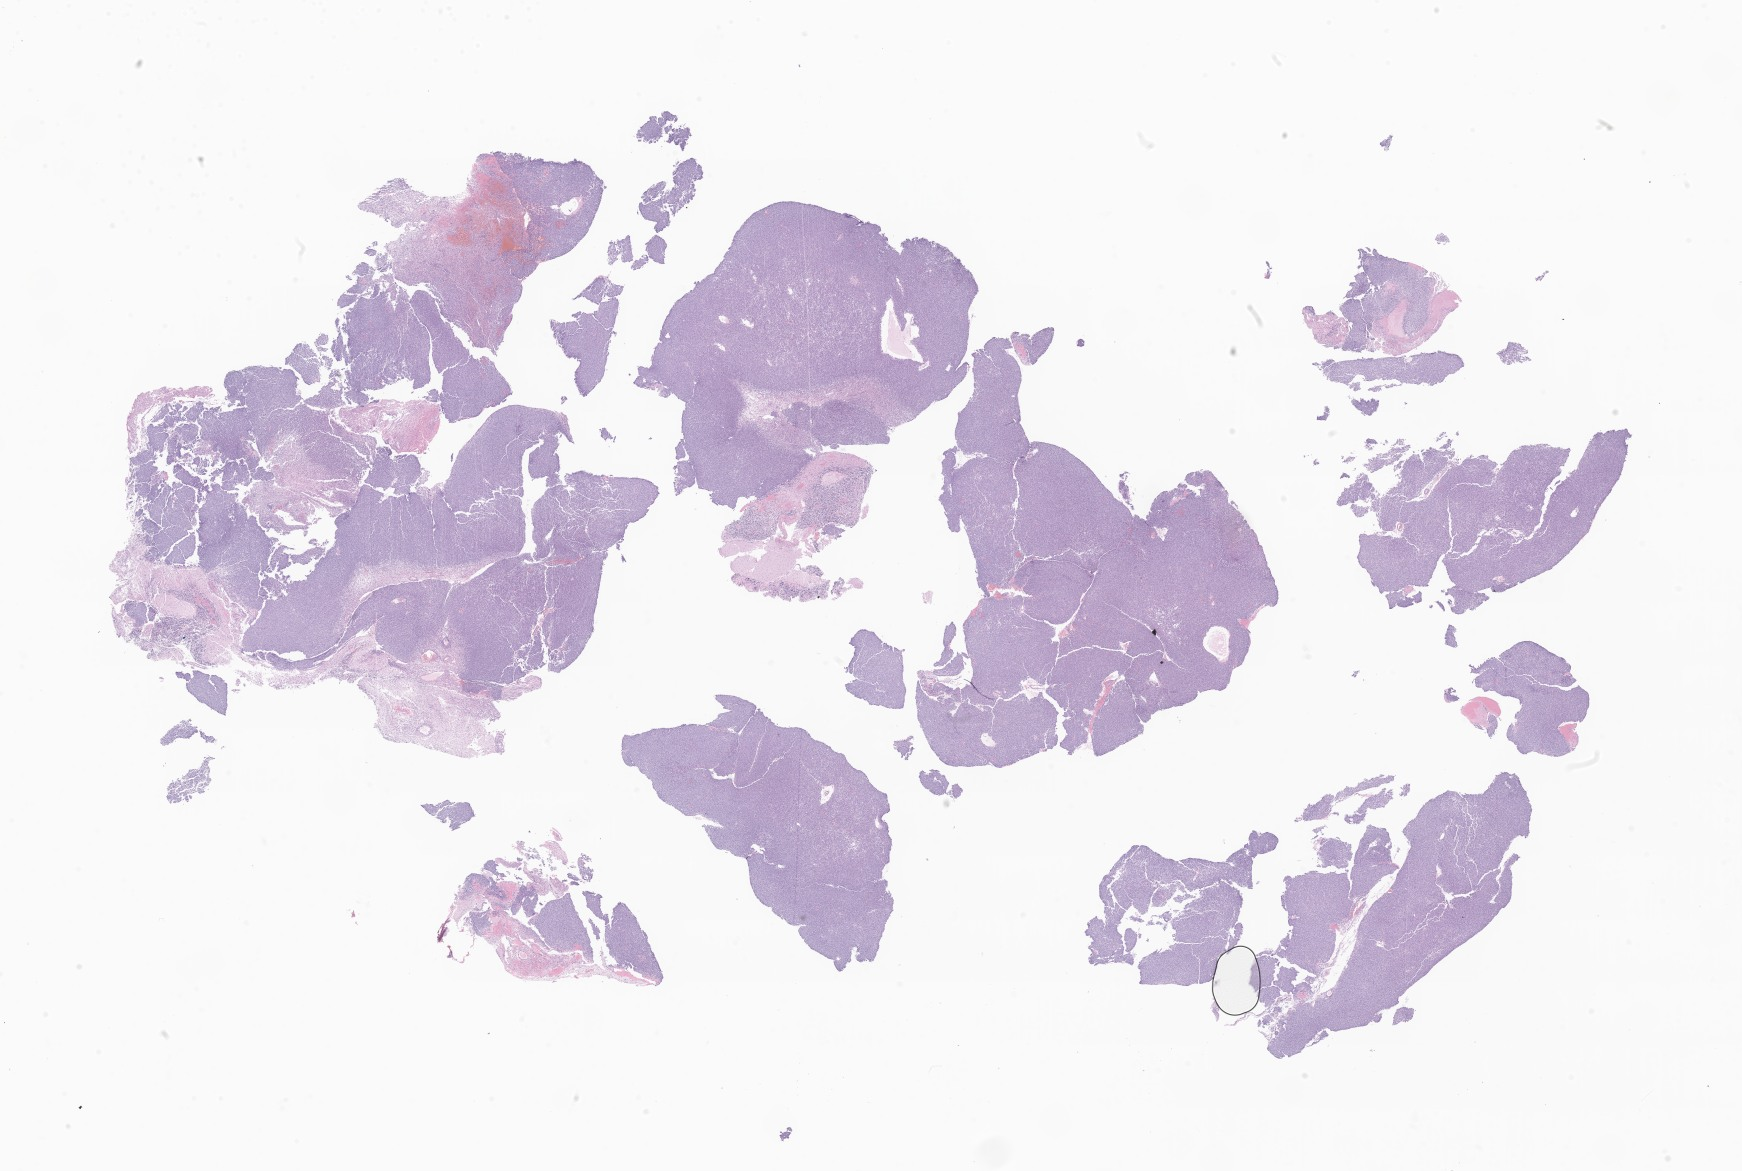
Whole-slide image, haematoxylin and eosin stain of tumor tissue from the brain, low-resolution overview of the scanned area, about 29.4 x 19.8 mm; FFPE section. Patient: male, age 41 months (3 years 5 months).
• recorded diagnosis: Neoplasm, uncertain whether benign or malignant